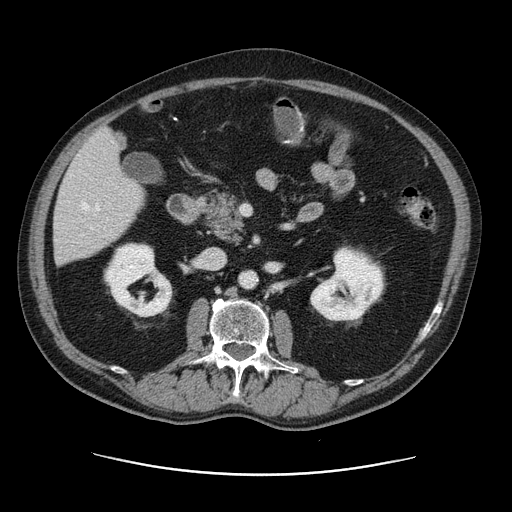
Contrast-enhanced abdominal CT, one axial slice; position 51 of 141 along the scan axis; intravenous contrast given; soft-tissue window (W 400 / L 40 HU); 512 × 512 image matrix, field of view 395 × 395 mm. Male patient, age 72 years. Case-level facts recorded for this patient, not image findings: diagnosis: colorectal cancer liver metastases, imaged before liver resection; multiple liver metastases: yes; largest metastasis: 5.4 cm; chemotherapy before resection: yes.
Outlined on this slice (expert manual segmentation):
- hepatic veins: bounding box (x1, y1, x2, y2) in pixels: (81, 202, 99, 229)
- liver: (54, 130, 145, 263)
- planned liver remnant (the part of the liver to remain after resection): (54, 169, 145, 264)